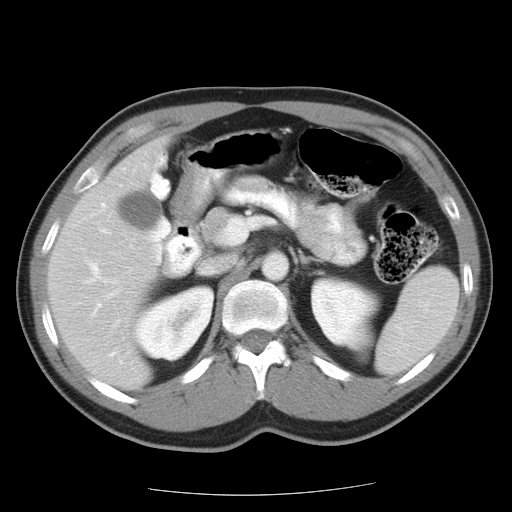
Contrast-enhanced abdominal CT, one axial slice. Position 9 of 22 along the scan axis. Intravenous contrast given. Soft-tissue window (W 400 / L 40 HU). 512 × 512 image matrix, field of view 359 × 359 mm. Male patient, age 41 years. Case-level facts recorded for this patient, not image findings: diagnosis: colorectal cancer liver metastases, imaged before liver resection; multiple liver metastases: no; largest metastasis: 2.7 cm; disease in both lobes: no.
Structures marked on this image (manually delineated by an expert):
- hepatic veins: bounding box (x1, y1, x2, y2) in pixels: (86, 204, 115, 356)
- liver: (49, 142, 162, 389)
- planned liver remnant (the part of the liver to remain after resection): (49, 142, 162, 376)
- portal vein (with intrahepatic branches): (103, 230, 109, 234)